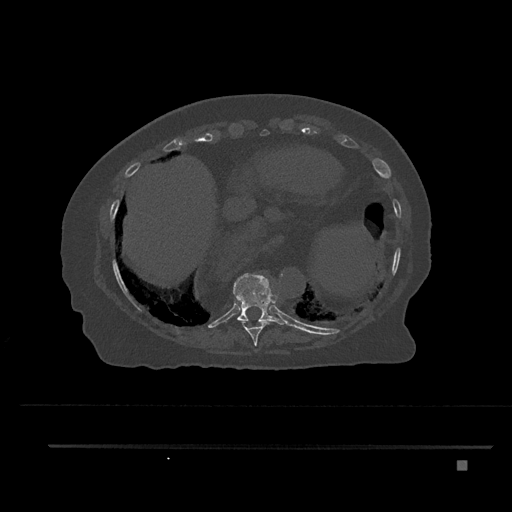
CT including the spine, one axial slice; position 375 of 797 along the scan axis; bone window (W 1800 / L 400 HU); 0.5 mm slice thickness; 512 × 512 image matrix. Patient: female, 76 years. Case-level facts recorded for this patient, not image findings: primary cancer: lung; vertebrae with lytic lesions (as recorded): T11, L3.
Structures marked on this image (semi-automatically segmented with operator editing):
- T10 vertebra: bounding box <233,273,289,326> (left, top, right, bottom; pixels)
- T9 vertebra: <238,320,269,346>